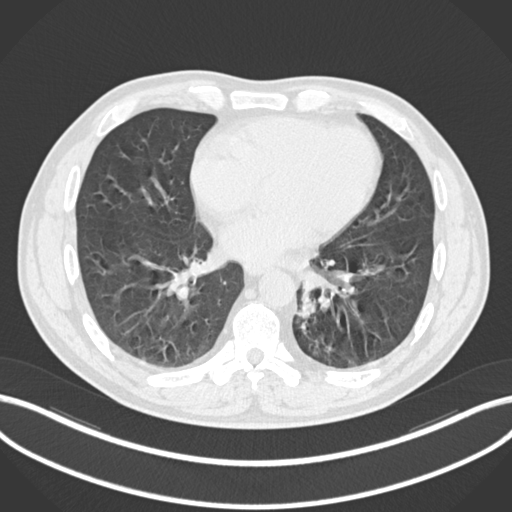
Chest CT, one axial slice. Slice 79 of 223 in the series (ordered by position). 120 kVp. Lung window (W 1500 / L -600 HU). 1 mm slice thickness. 512 × 512 image matrix, field of view 400 × 400 mm. Patient: male, 50 years. From the clinical record (not read from this slice): clinical TNM (as recorded): T2a N3 M0.
Outlined on this slice (bounding box drawn by a radiologist):
- lung tumour (recorded histology: squamous cell carcinoma): bounding box <291,285,320,321> (left, top, right, bottom; pixels)